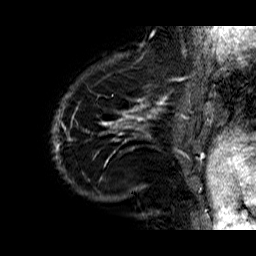
Breast MRI (dynamic contrast-enhanced), one sagittal slice. Slice 6 of 60 in the series (ordered by position). Dynamic contrast-enhanced series, time point 2 of 6 at this slice position (early post-contrast). 1.5 T. TE 6.3 ms, TR 32.9 ms. 256 × 256 image matrix, field of view 200 × 200 mm. Female patient. Case-level facts recorded for this patient, not image findings: setting: breast cancer imaged before/during neoadjuvant chemotherapy; receptor status: HR-positive, HER2-negative.
Structures marked on this image (semi-automatic segmentation, software-assisted and operator-edited):
- analysis volume of interest (the breast-tissue region the enhancement analysis was run in; not a lesion): bounding box [x1, y1, x2, y2] px = [52, 74, 176, 210]
- tumour enhancement mask (voxels above the 100 % enhancement threshold inside the analysis volume of interest): [52, 78, 173, 197]